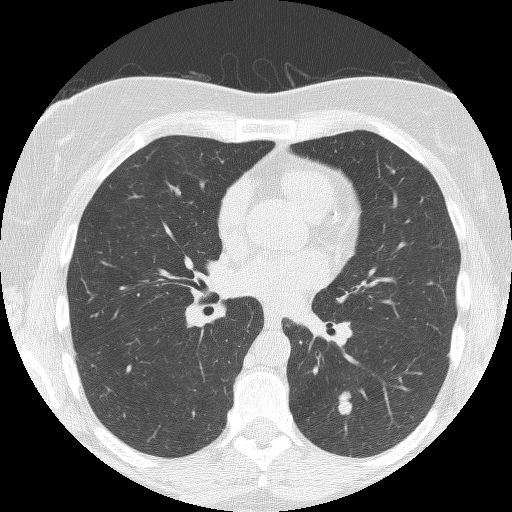
Low-dose screening chest CT, axial slice, second annual screen, lung window (W 1500 / L -600 HU), lung (sharp) reconstruction kernel (BONE), slice 72 of 150 in the series. Female participant, aged 60 years at enrolment.
Lesion marked by an expert reader, bounding box <319,383,360,425> (left, top, right, bottom; pixels). Reader record for this screening exam (exam-level; its link to the box is not recorded): non-calcified nodule or mass ≥4 mm, left lower lobe, 16 × 7 mm, smooth margins, soft tissue attenuation, pre-existing on the prior screen: no. Official screen result: positive, other. Lung cancer was diagnosed 54 days after this screen: small cell carcinoma, NOS, left lower lobe, stage IIA (AJCC 6th edition), 12 mm at pathology.